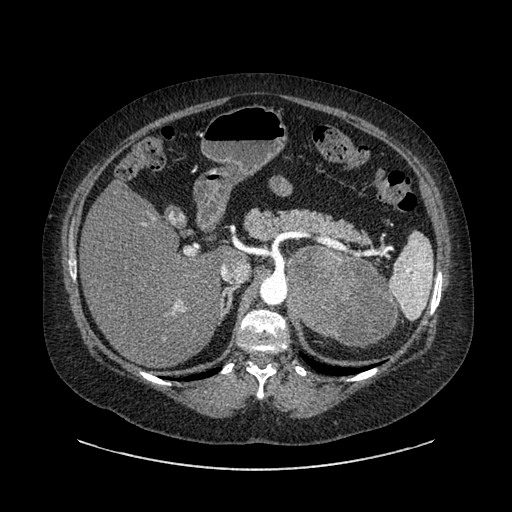
Contrast-enhanced abdominal CT, one axial slice; position 586 of 769 along the scan axis; reconstruction kernel SOFT; intravenous contrast given; soft-tissue window (W 400 / L 40 HU); 0.62 mm slice thickness; 512 × 512 image matrix, field of view 460 × 460 mm. Female patient, age 61 years. From the clinical record (not read from this slice): diagnosis: adrenocortical carcinoma; tumour side: left adrenal.
Structures marked on this image (semi-automatic segmentation, software-assisted and operator-edited):
- mass: bounding box <287,249,397,346> (left, top, right, bottom; pixels)